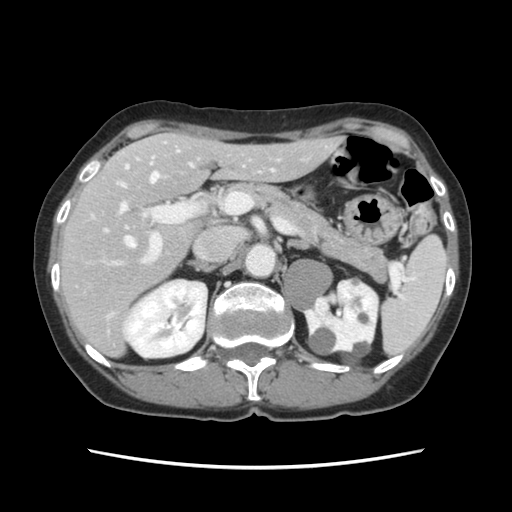
Contrast-enhanced abdominal CT, one axial slice. Slice 74 of 120 in the series (ordered by position). Intravenous contrast given. Soft-tissue window (W 400 / L 40 HU). 2.5 mm slice thickness. 512 × 512 image matrix, field of view 330 × 330 mm. Female patient, age 70 years. Case-level facts recorded for this patient, not image findings: diagnosis: colorectal cancer liver metastases, imaged before liver resection; multiple liver metastases: no; largest metastasis: 2.5 cm; chemotherapy before resection: yes.
Annotated regions visible in this slice (outlined manually by an expert reader):
- hepatic veins: bounding box (x1, y1, x2, y2) in pixels: (105, 151, 178, 247)
- liver: (61, 133, 338, 355)
- planned liver remnant (the part of the liver to remain after resection): (91, 133, 339, 282)
- portal vein (with intrahepatic branches): (110, 142, 232, 317)